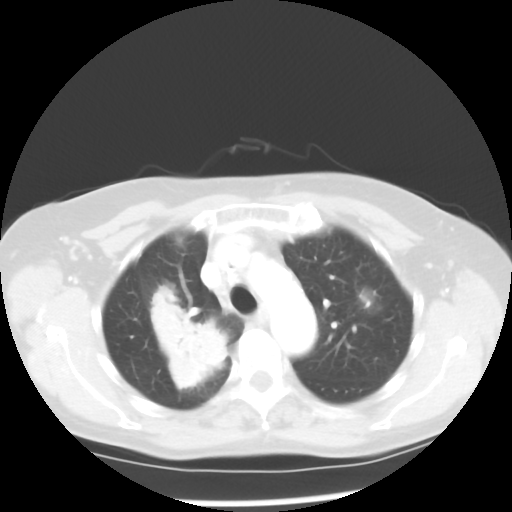
Chest CT, one axial slice; position 38 of 52 along the scan axis; reconstruction kernel STANDARD; 100 kVp; lung window (W 1500 / L -600 HU); 512 × 512 image matrix, field of view 328 × 328 mm. Female patient, age 60 years. From the clinical record (not read from this slice): clinical TNM (as recorded): T2 N1 M1a.
Annotated regions visible in this slice (bounding box drawn by a radiologist):
- lung tumour (recorded histology: adenocarcinoma): bounding box [x1, y1, x2, y2] px = [145, 283, 232, 395]